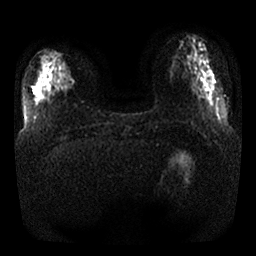
Breast MRI, one axial slice; position 8 of 32 along the scan axis; diffusion-weighted series; image 2 of 4 stored at this slice position (different b-values; order by instance number); 1.5 T; 4 mm slice thickness; 256 × 256 image matrix, field of view 350 × 350 mm. Female patient.
Outlined on this slice (manually delineated by an expert):
- tumour on diffusion-weighted imaging: box from (x=63, y=76) to (x=72, y=89) px